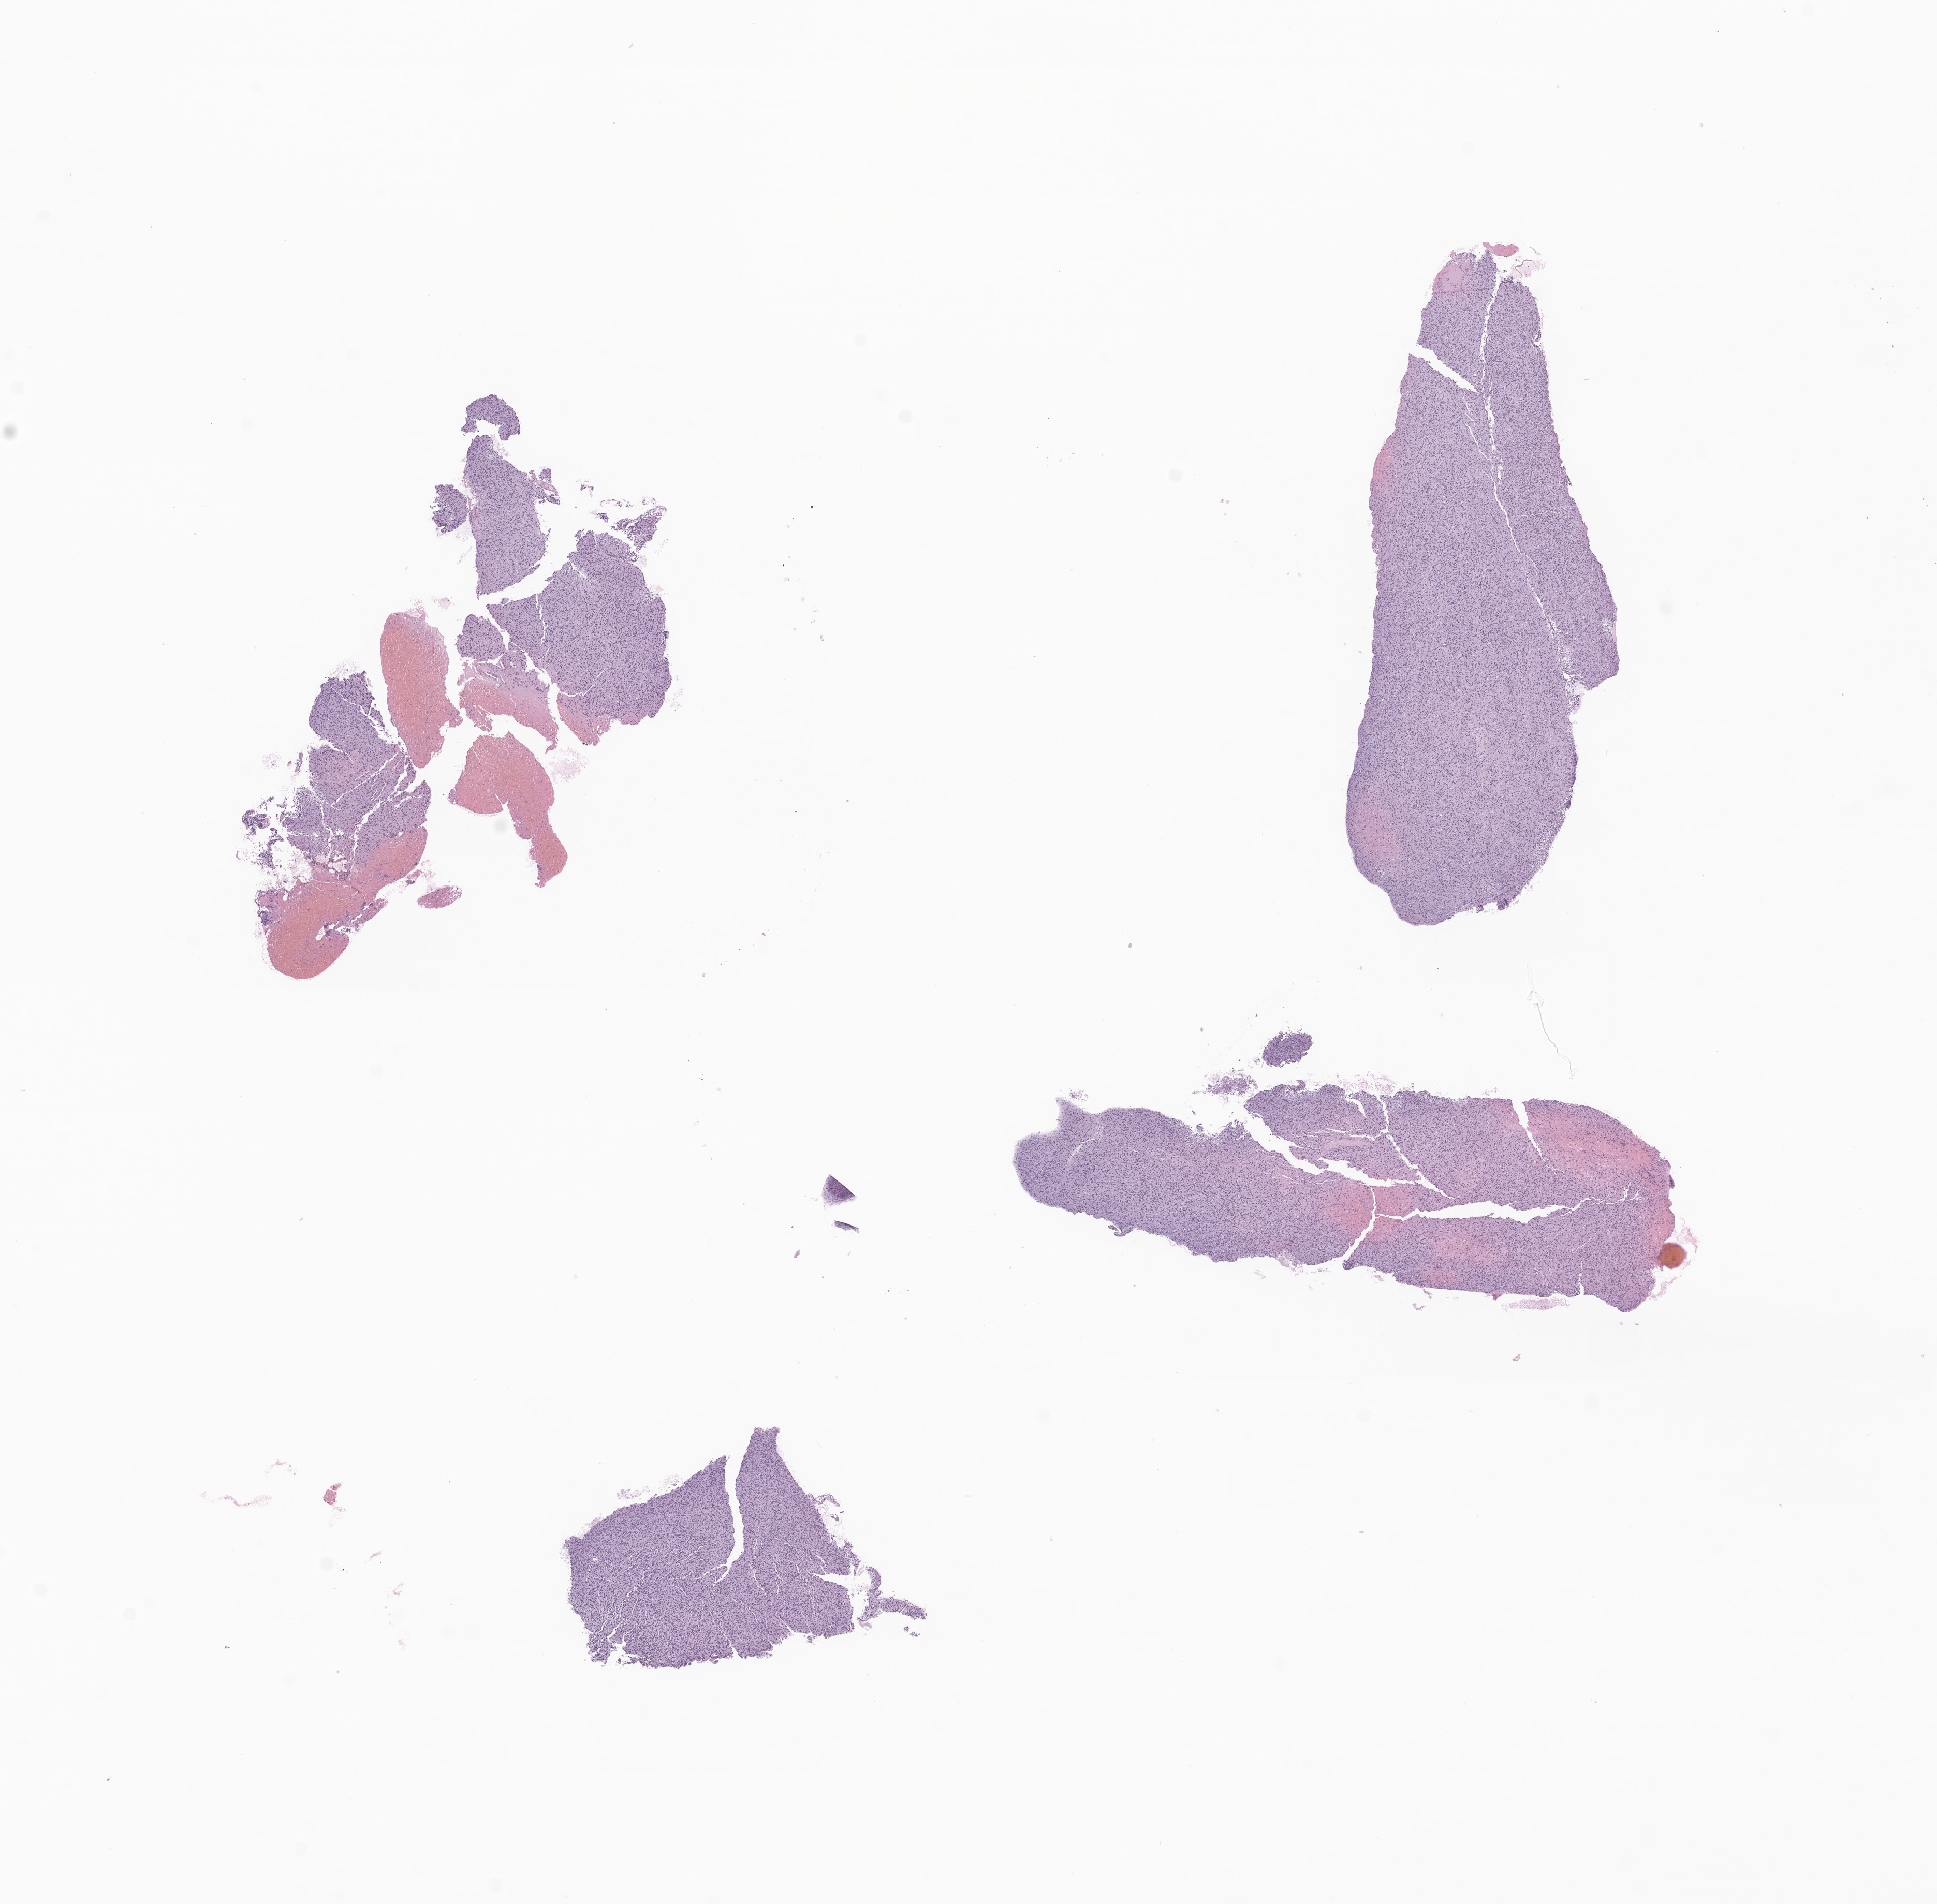
Digitized hematoxylin and eosin (H&E)-stained section of tumor tissue from the brain — low-resolution overview of the scanned area, about 15.8 x 15.5 mm, formalin-fixed, paraffin-embedded (FFPE) tissue. Male patient, age 209 months (17 years 5 months).
* diagnosis (ICD-O-3 morphology term): Glioma, malignant